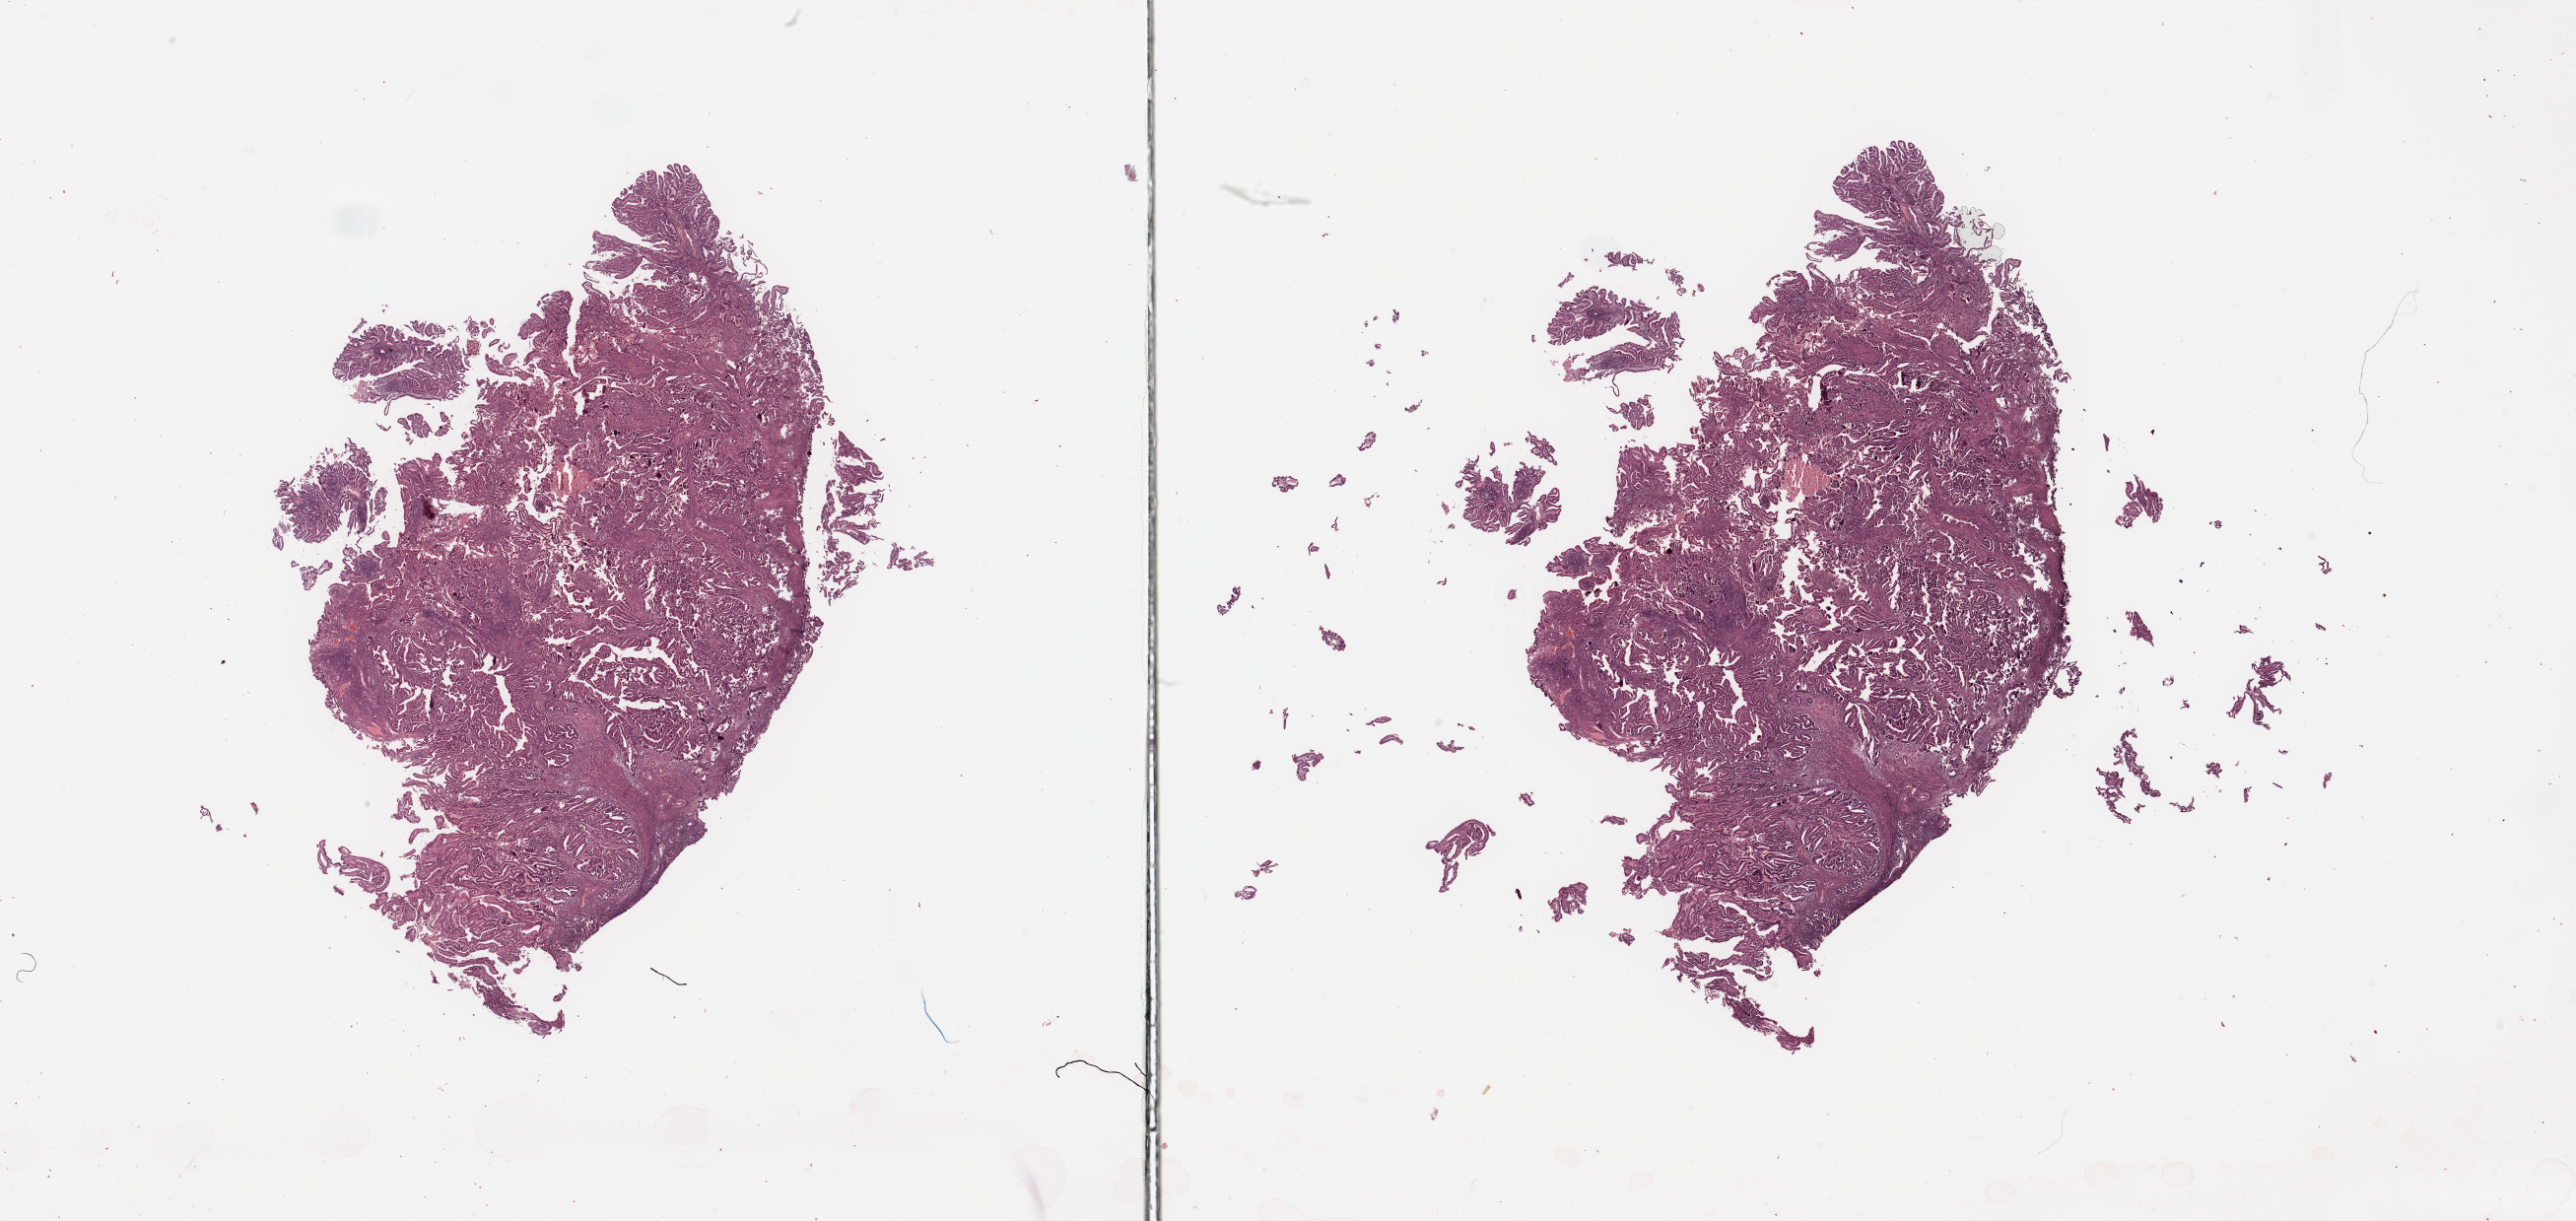
H&E whole-slide image, a low-resolution overview of the entire scanned area, about 41.3 x 19.6 mm; tumour tissue sample, sampled site: uterus. 54-year-old female patient. Histologic grade: G2 (moderately differentiated). Pathologist review of this section (percent, as recorded): tumour nuclei 90%, necrosis 2%.
• histologic diagnosis: Endometrioid adenocarcinoma, NOS
• AJCC pathologic stage: I